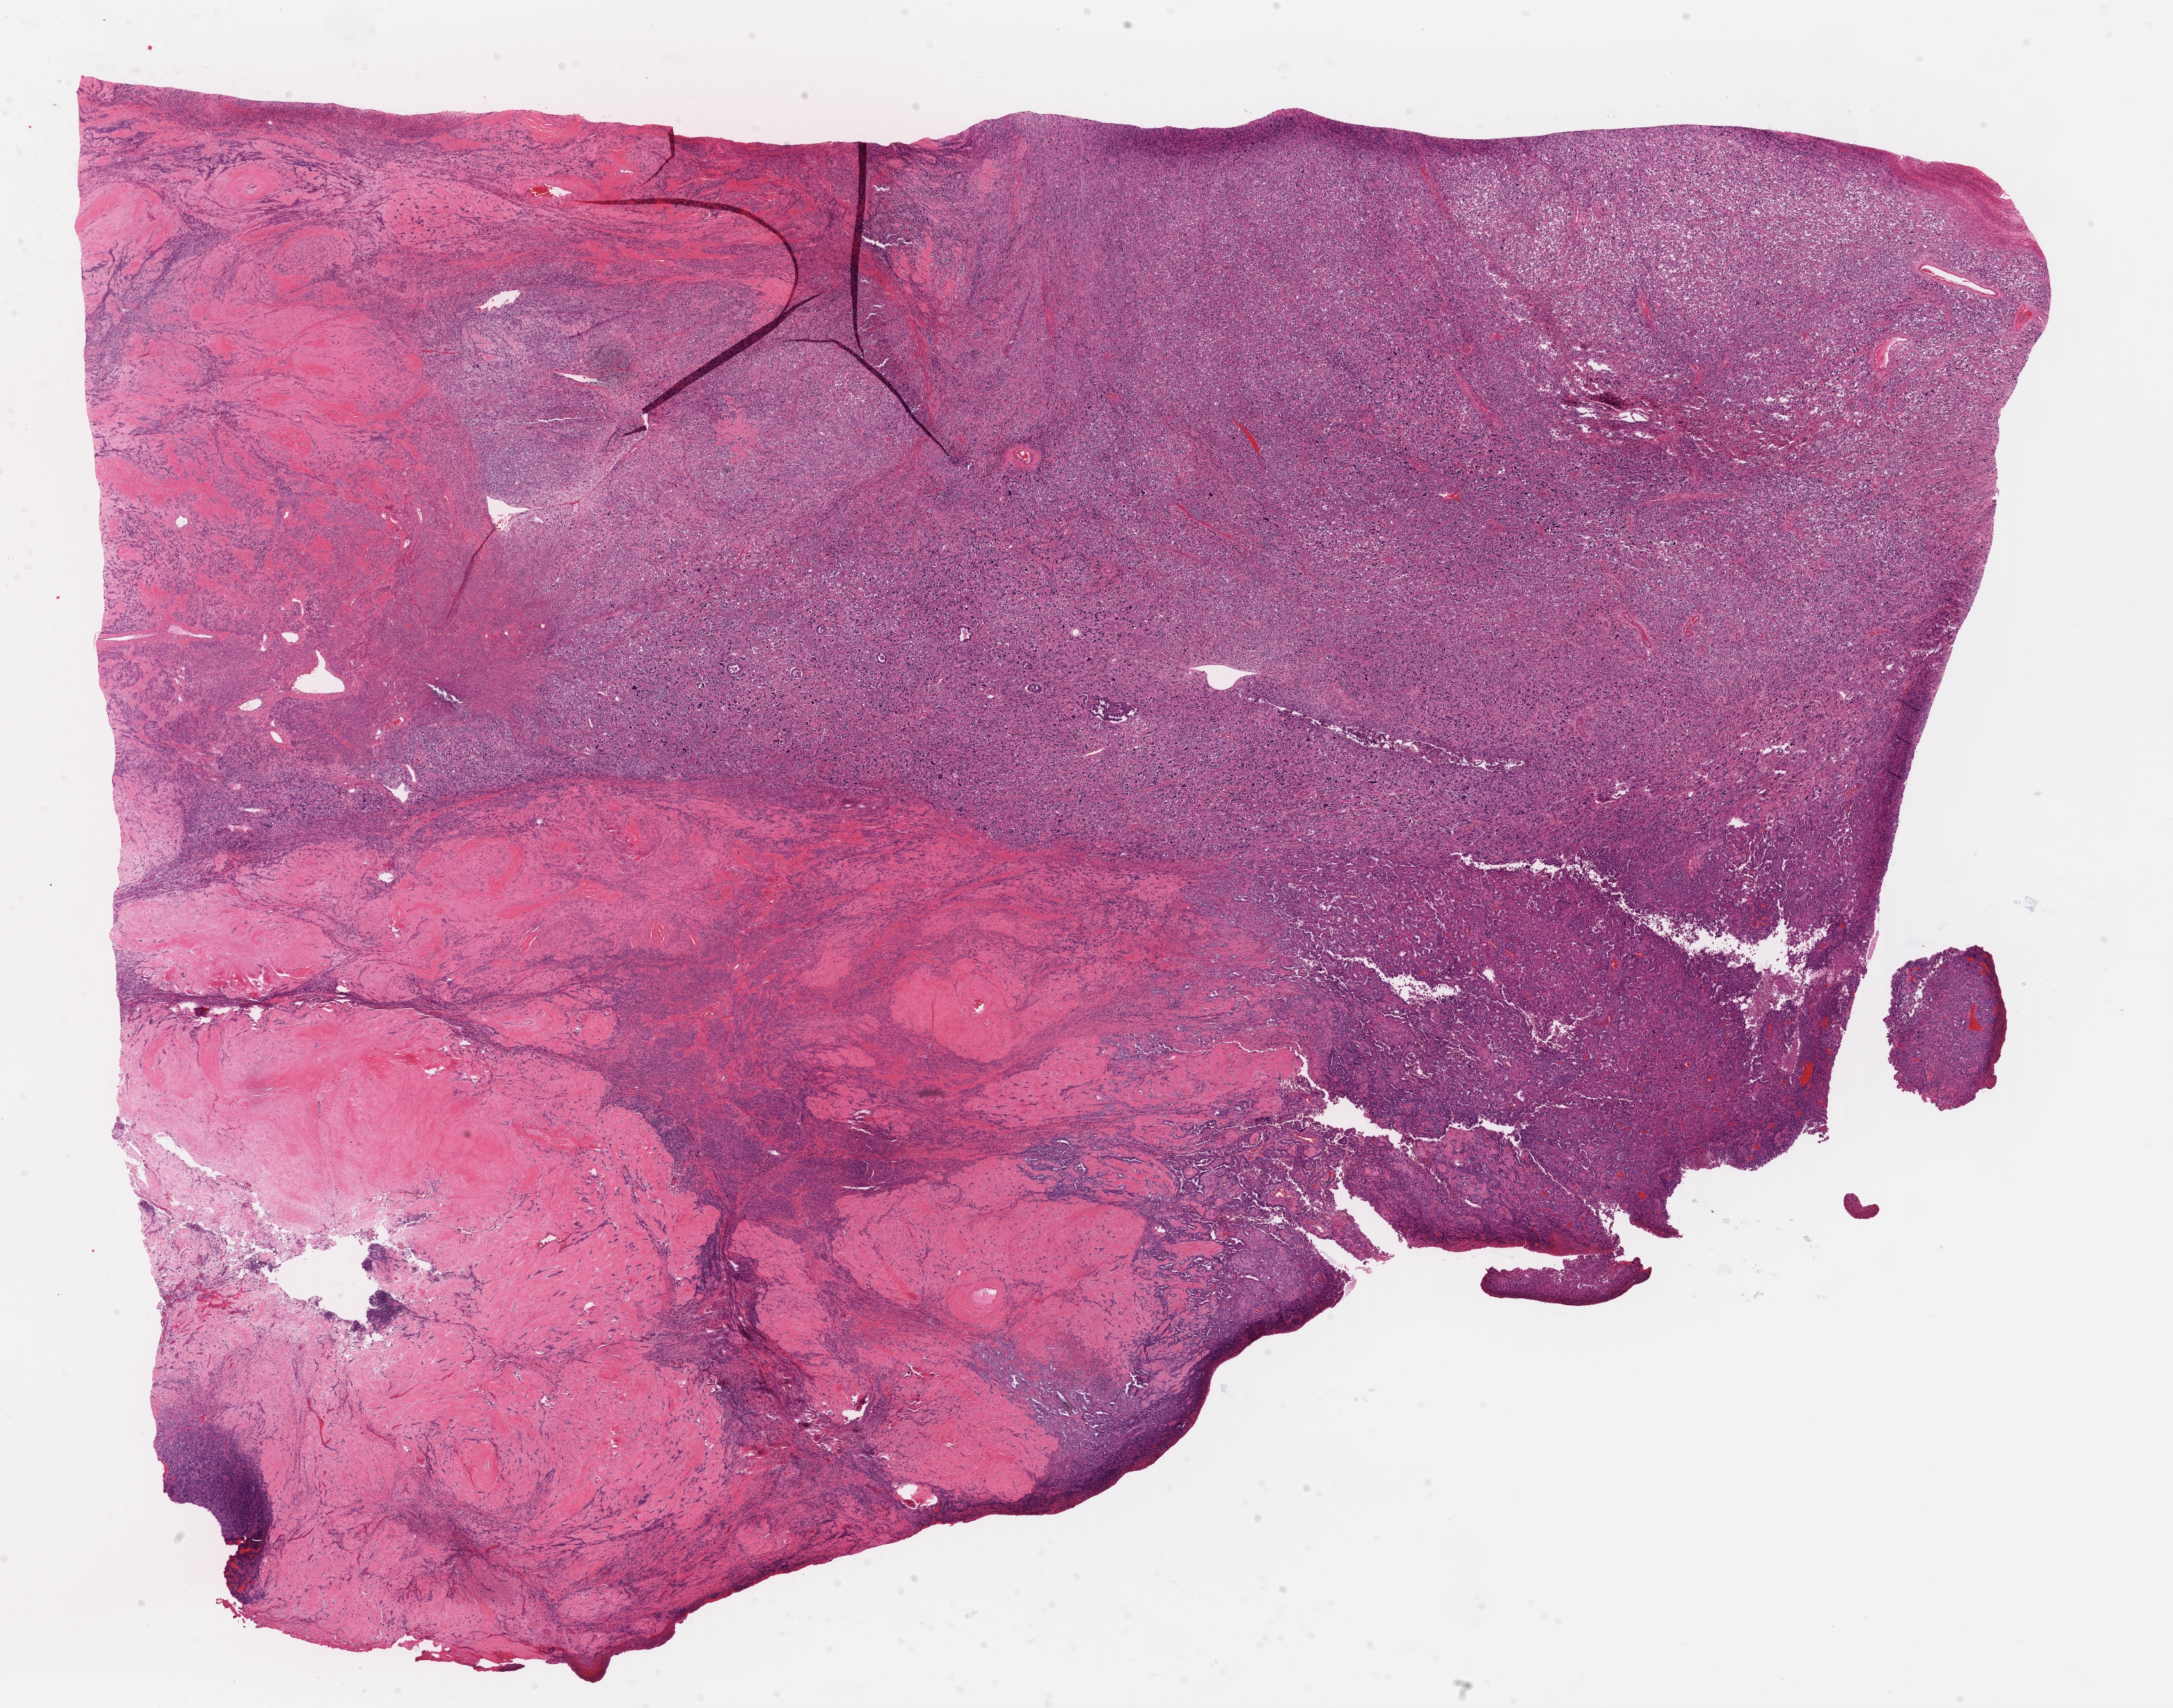
Hematoxylin and eosin (H&E) stained whole-slide image, shown as a low-resolution overview of the whole scanned area (about 24.6 x 19.3 mm, slide scanned at 40x); formalin-fixed paraffin-embedded (FFPE) diagnostic section; uterus, primary tumour sample. Female patient; age at initial diagnosis 67 years.
* pathologic diagnosis: Mullerian mixed tumor (endometrium)
* FIGO stage: IIIC